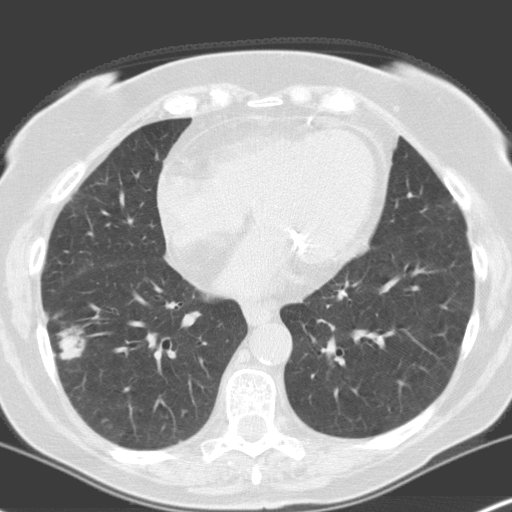
Chest CT (low-dose screening protocol), one axial image. Baseline annual screen. Lung window (W 1500 / L -600 HU). 3.2 mm slice thickness. Standard (soft-tissue) reconstruction kernel (C). 512 × 512 image matrix. Female, age 70 years at enrolment. Current smoker at enrolment.
Expert reader's lesion annotation, bounding box <35,309,100,378> (left, top, right, bottom; pixels). The screening reader recorded 4 non-calcified nodules or masses ≥4 mm on this exam (right lower lobe, right upper lobe, left upper lobe, left upper lobe); which of them this box marks is not recorded. Participant outcome: lung cancer diagnosed 28 days after this screen — adenocarcinoma, NOS, right lower lobe, moderately differentiated (G2), stage IV (AJCC 6th edition), 28 mm at pathology.